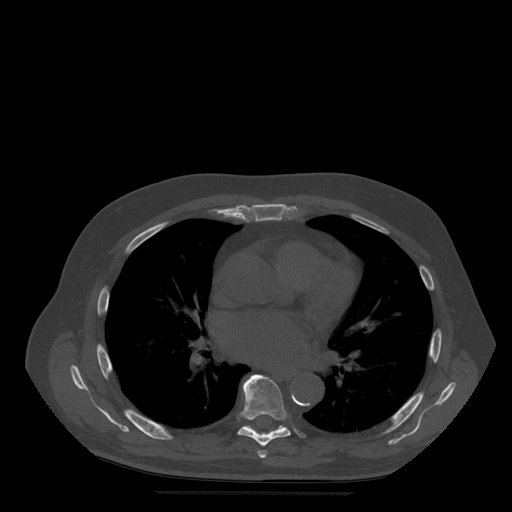
CT including the spine, one axial slice. Slice 331 of 522 in the series (ordered by position). Bone window (W 1800 / L 400 HU). 1.25 mm slice thickness. 512 × 512 image matrix, field of view 420 × 420 mm. Patient age 72 years. Case-level facts recorded for this patient, not image findings: primary cancer: prostate.
Structures marked on this image (semi-automatic segmentation, software-assisted and operator-edited):
- T6 vertebra: bounding box [x1, y1, x2, y2] px = [257, 451, 267, 459]
- T7 vertebra: [238, 375, 291, 447]
- T8 vertebra: [245, 426, 286, 432]